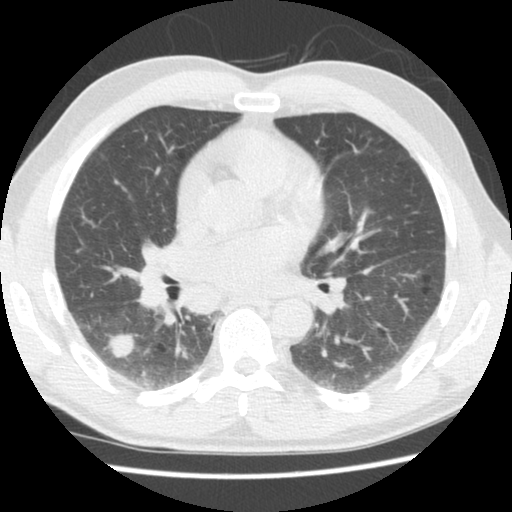
Low-dose screening chest CT, one axial slice. Position 77 of 133 along the scan axis. 140 kVp. Lung window (W 1500 / L -600 HU). 2.5 mm slice thickness. 512 × 512 image matrix.
Structures marked on this image (outlined manually by an expert reader):
- lesion 1 (tumor, lower lobe of right lung): bounding box (x1, y1, x2, y2) in pixels: (108, 333, 136, 359)